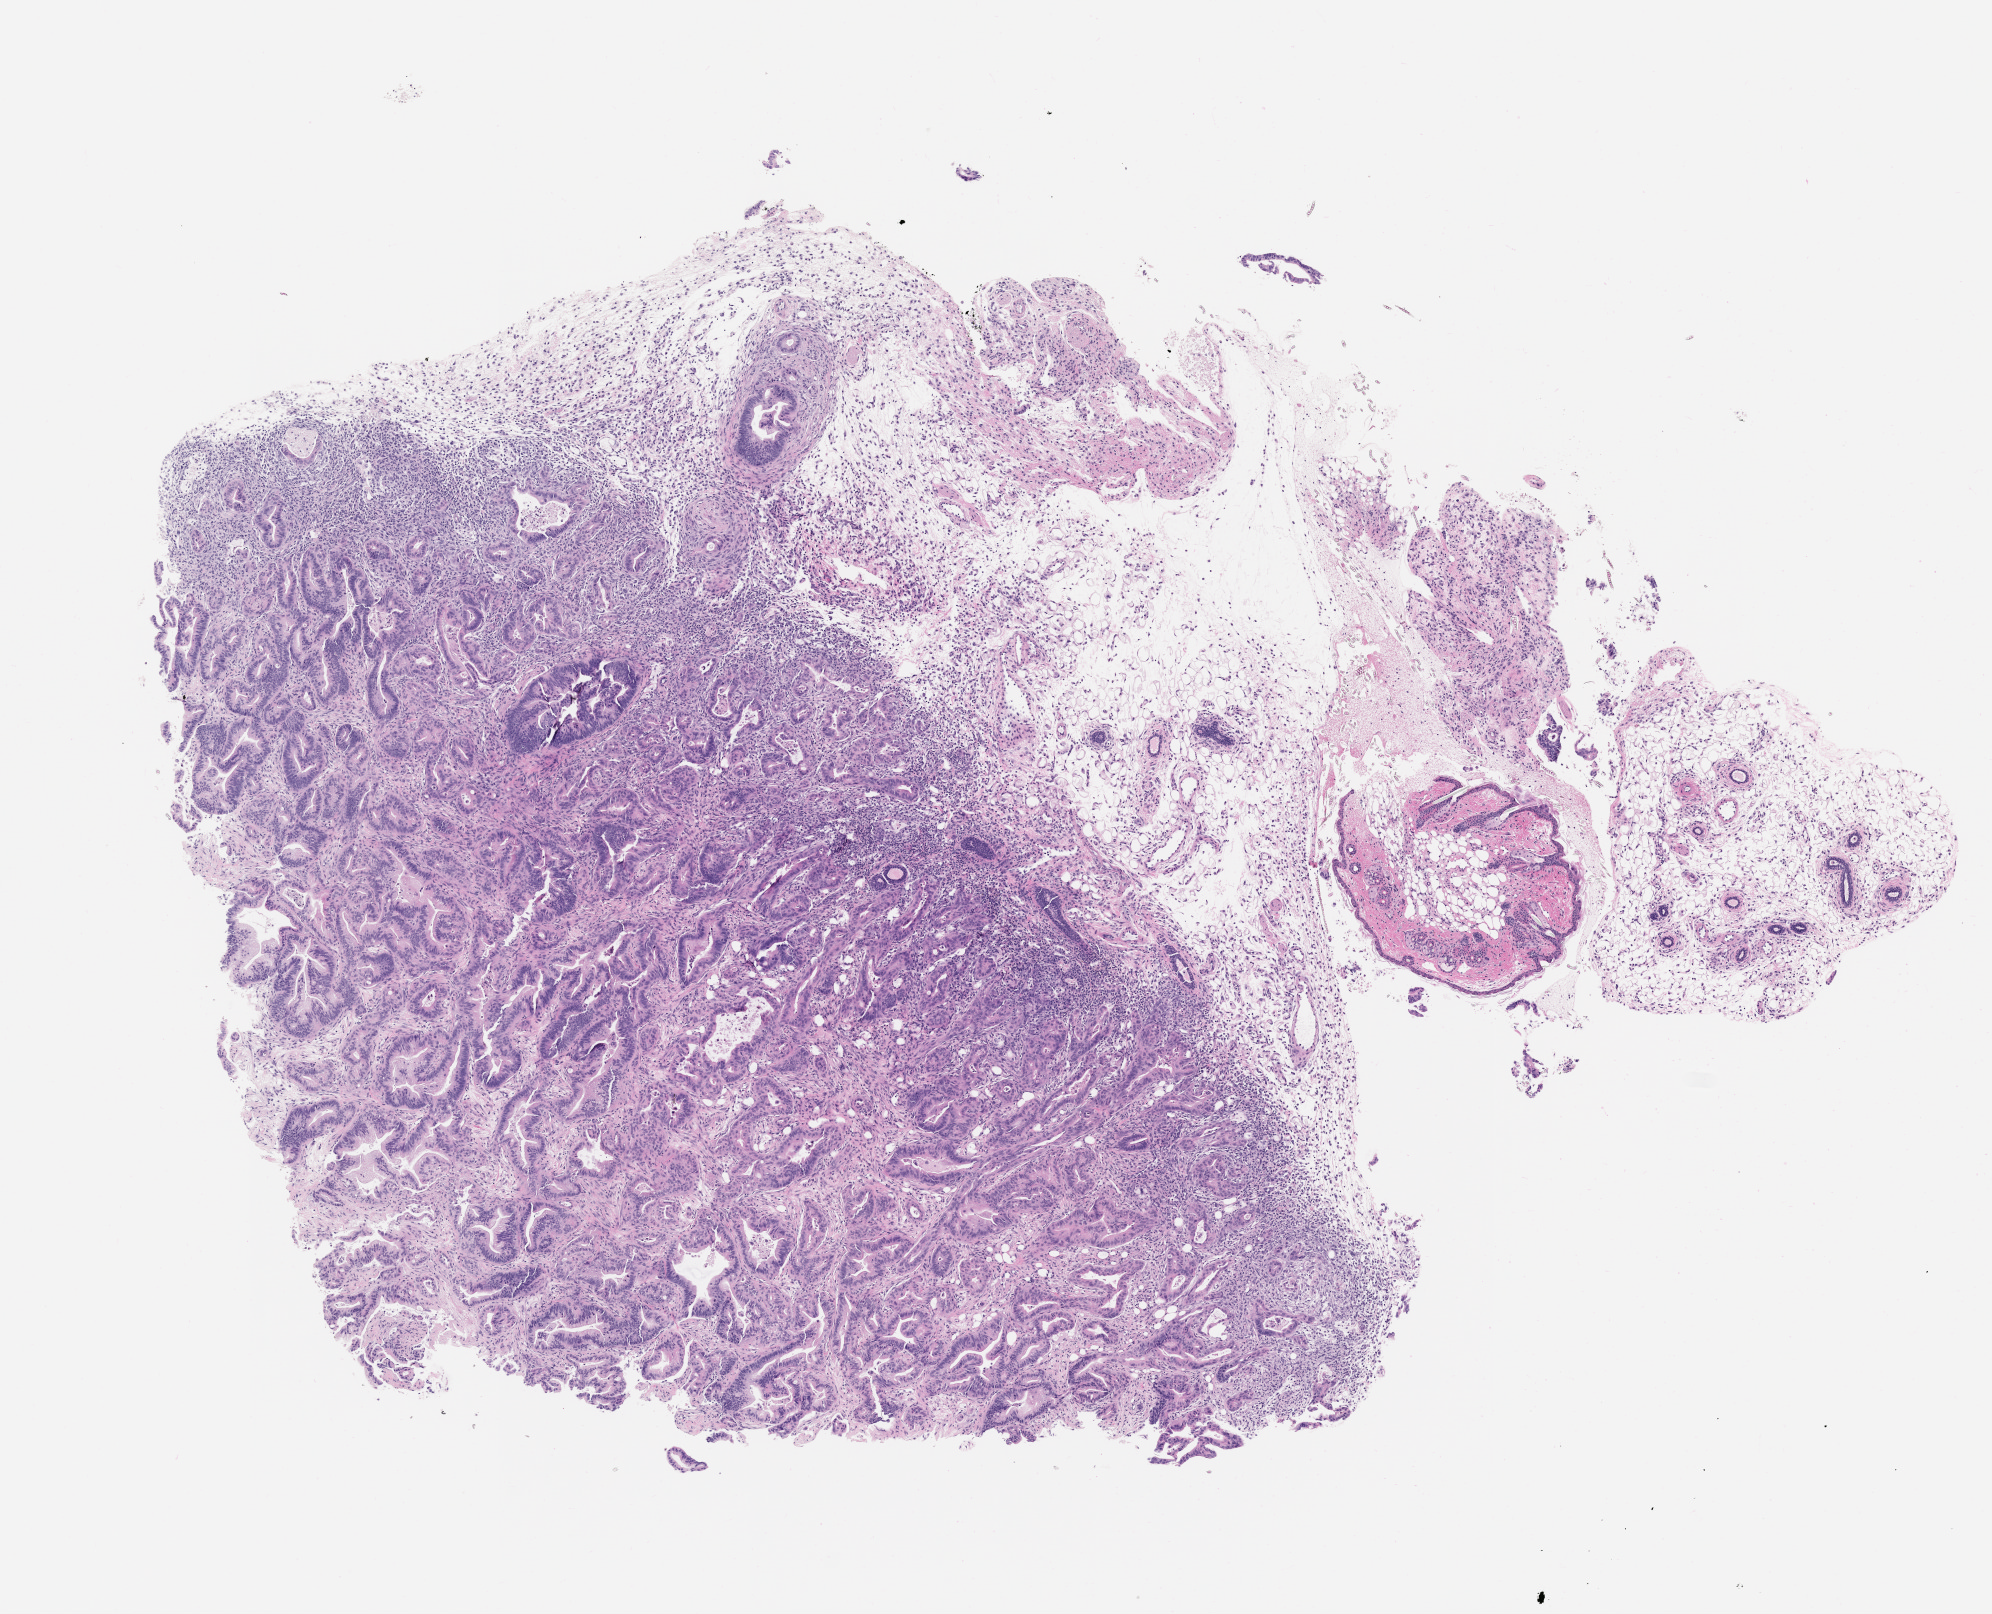
Whole-slide image, haematoxylin and eosin: patient-derived xenograft (human tumor grown in a mouse), passage 0 — low-resolution overview of the scanned area, about 8.0 x 6.5 mm; FFPE section; originating tumor site category: pancreas.
Originating patient diagnosis: Pancreatic Adenocarcinoma.